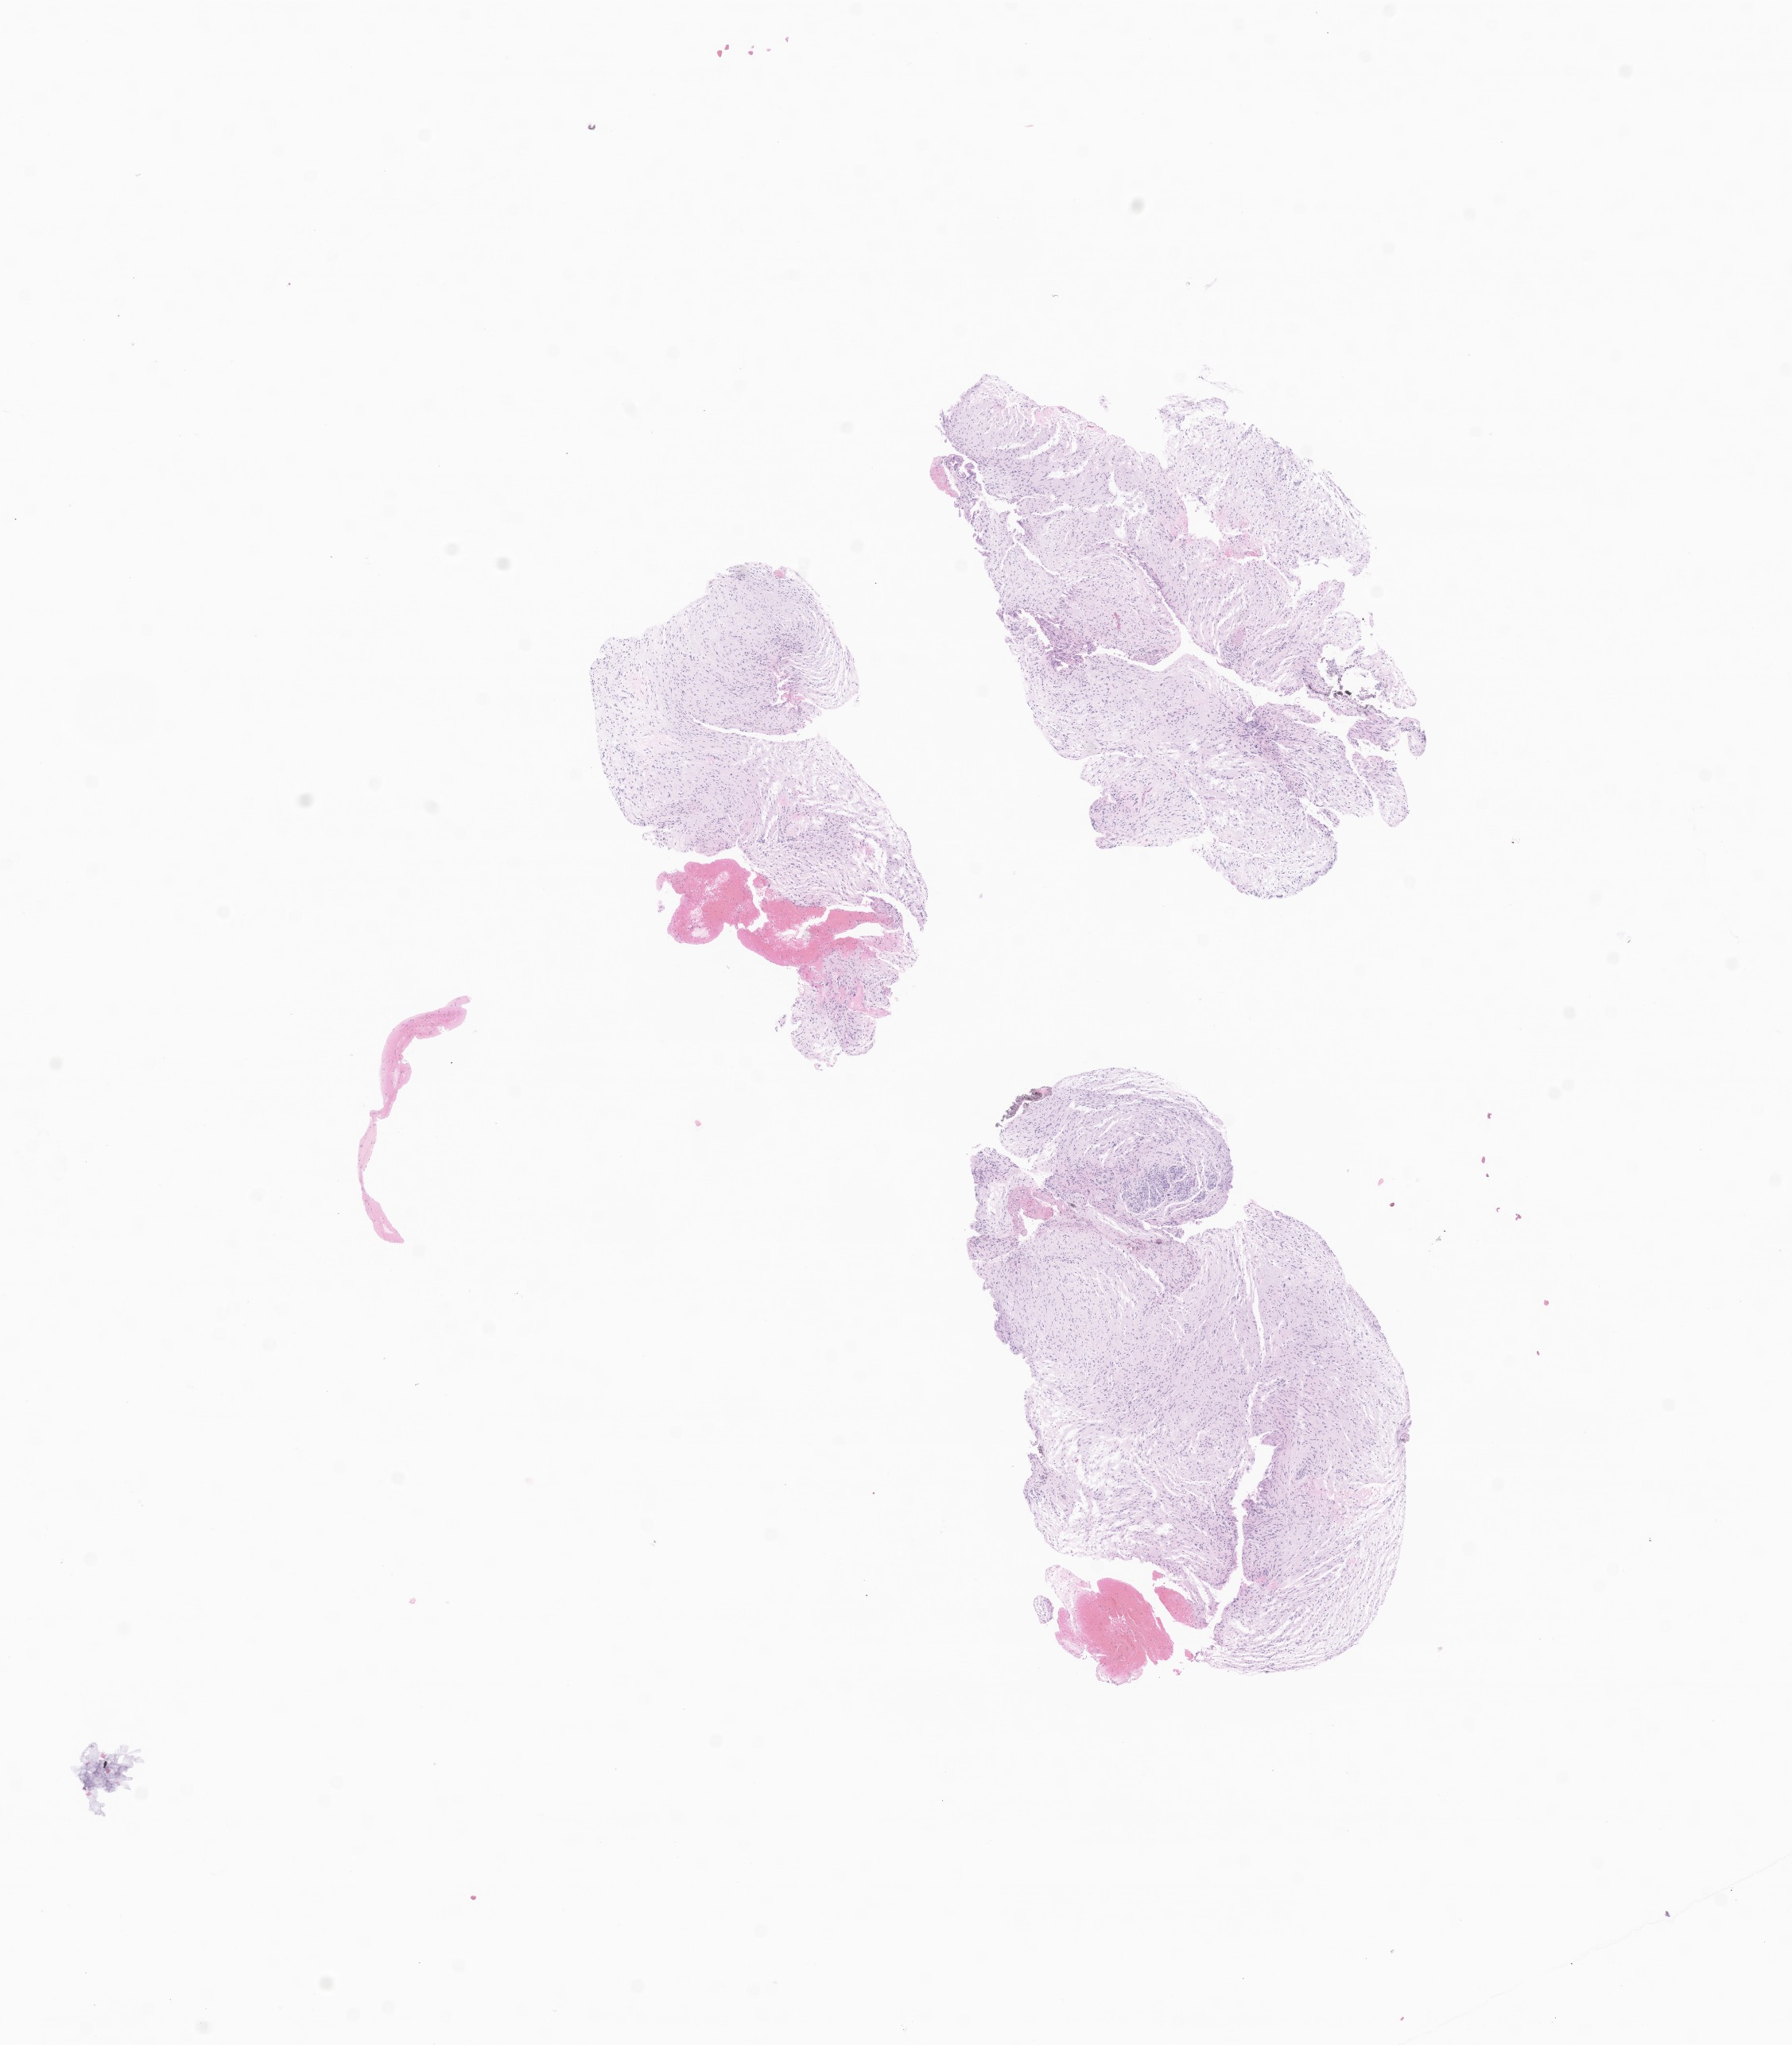
Digitized haematoxylin and eosin-stained section of tumor tissue from the brain, low-resolution overview of the scanned area, about 9.5 x 10.8 mm, formalin-fixed, paraffin-embedded (FFPE) tissue. Patient male; age 131 months (10 years 11 months).
Diagnosis (ICD-O-3 morphology term): Pilocytic astrocytoma.